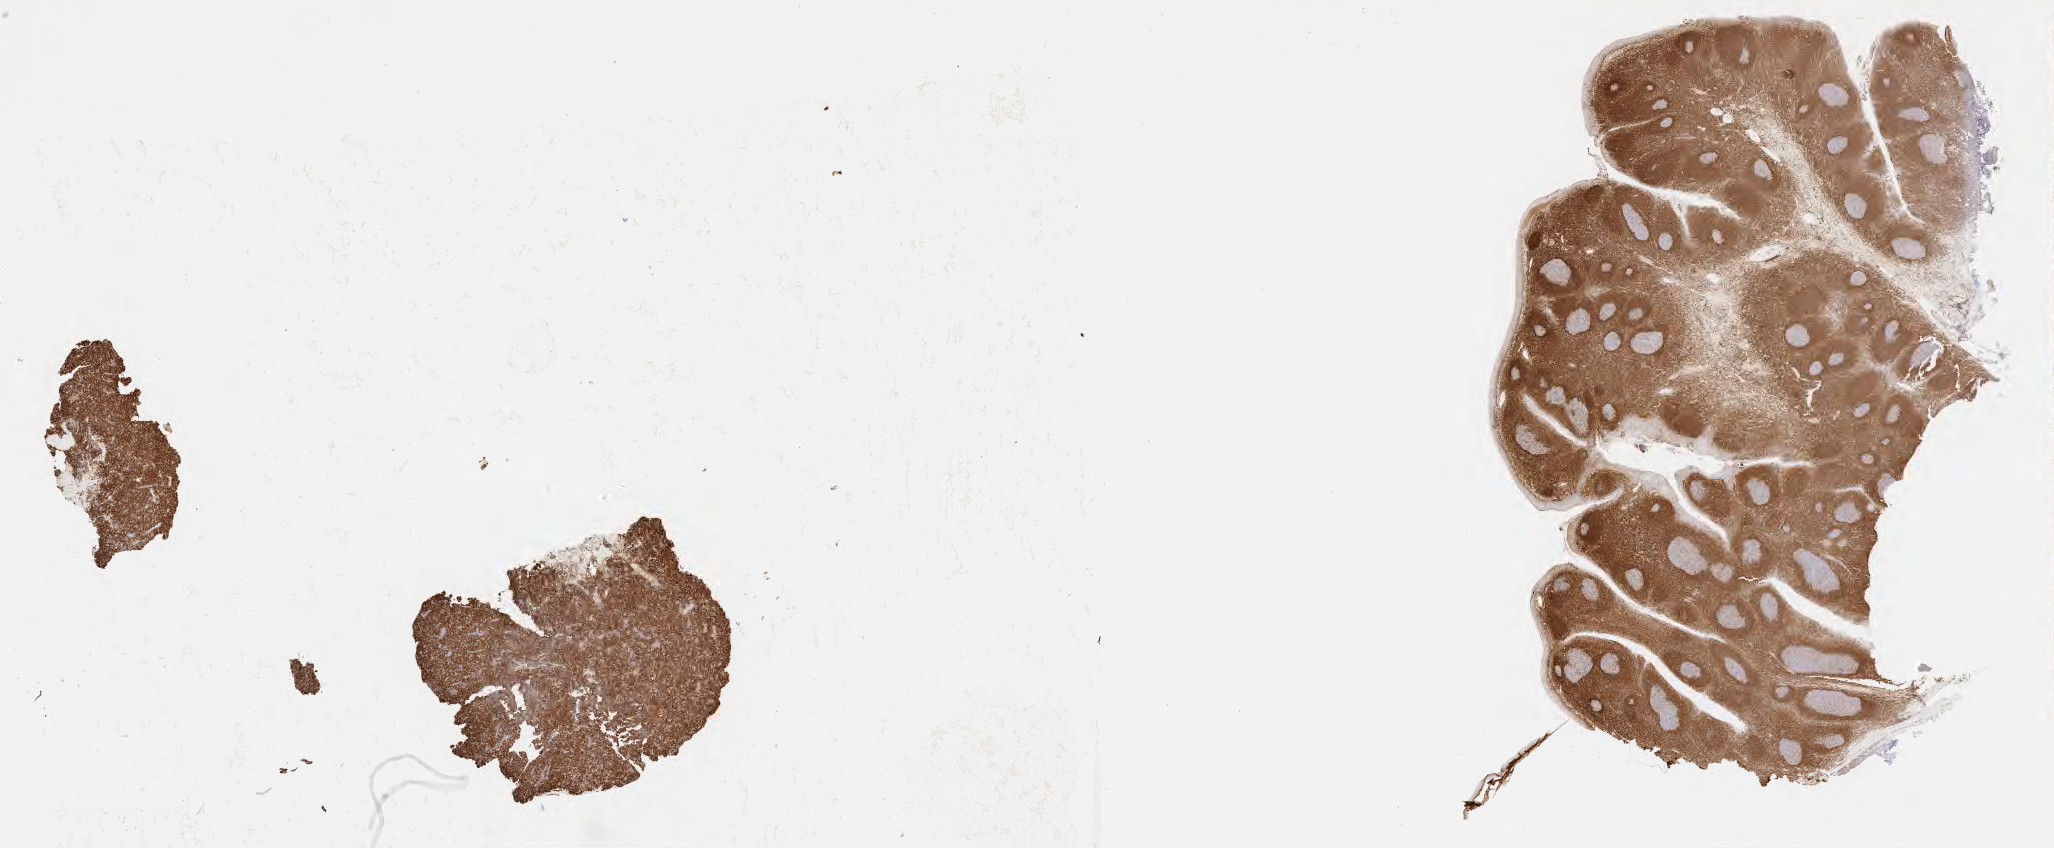
Immunohistochemistry (IHC) whole-slide image stained for BCL2 — a low-resolution overview of the entire scanned area, about 33.2 x 13.7 mm, specimen: tumor tissue, anatomic site: lymph node. Patient: female, 51 years old.
- diagnosis: Diffuse large B-cell lymphoma, NOS